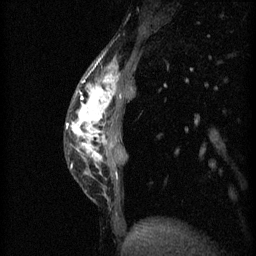
Breast MRI (dynamic contrast-enhanced), one sagittal slice; position 14 of 60 along the scan axis; 3 images stored at this slice position (order not interpretable as contrast timing); 1.5 T; TE 4.2 ms, TR 11 ms; 2 mm slice thickness; 256 × 256 image matrix. Female patient, age 40 years.
Annotated regions visible in this slice (semi-automatic segmentation, software-assisted and operator-edited):
- analysis volume of interest (the breast-tissue region the enhancement analysis was run in; not a lesion): bounding box [x1, y1, x2, y2] px = [67, 56, 135, 199]
- tumour enhancement mask (voxels above the 70 % enhancement threshold inside the analysis volume of interest): [67, 66, 118, 169]